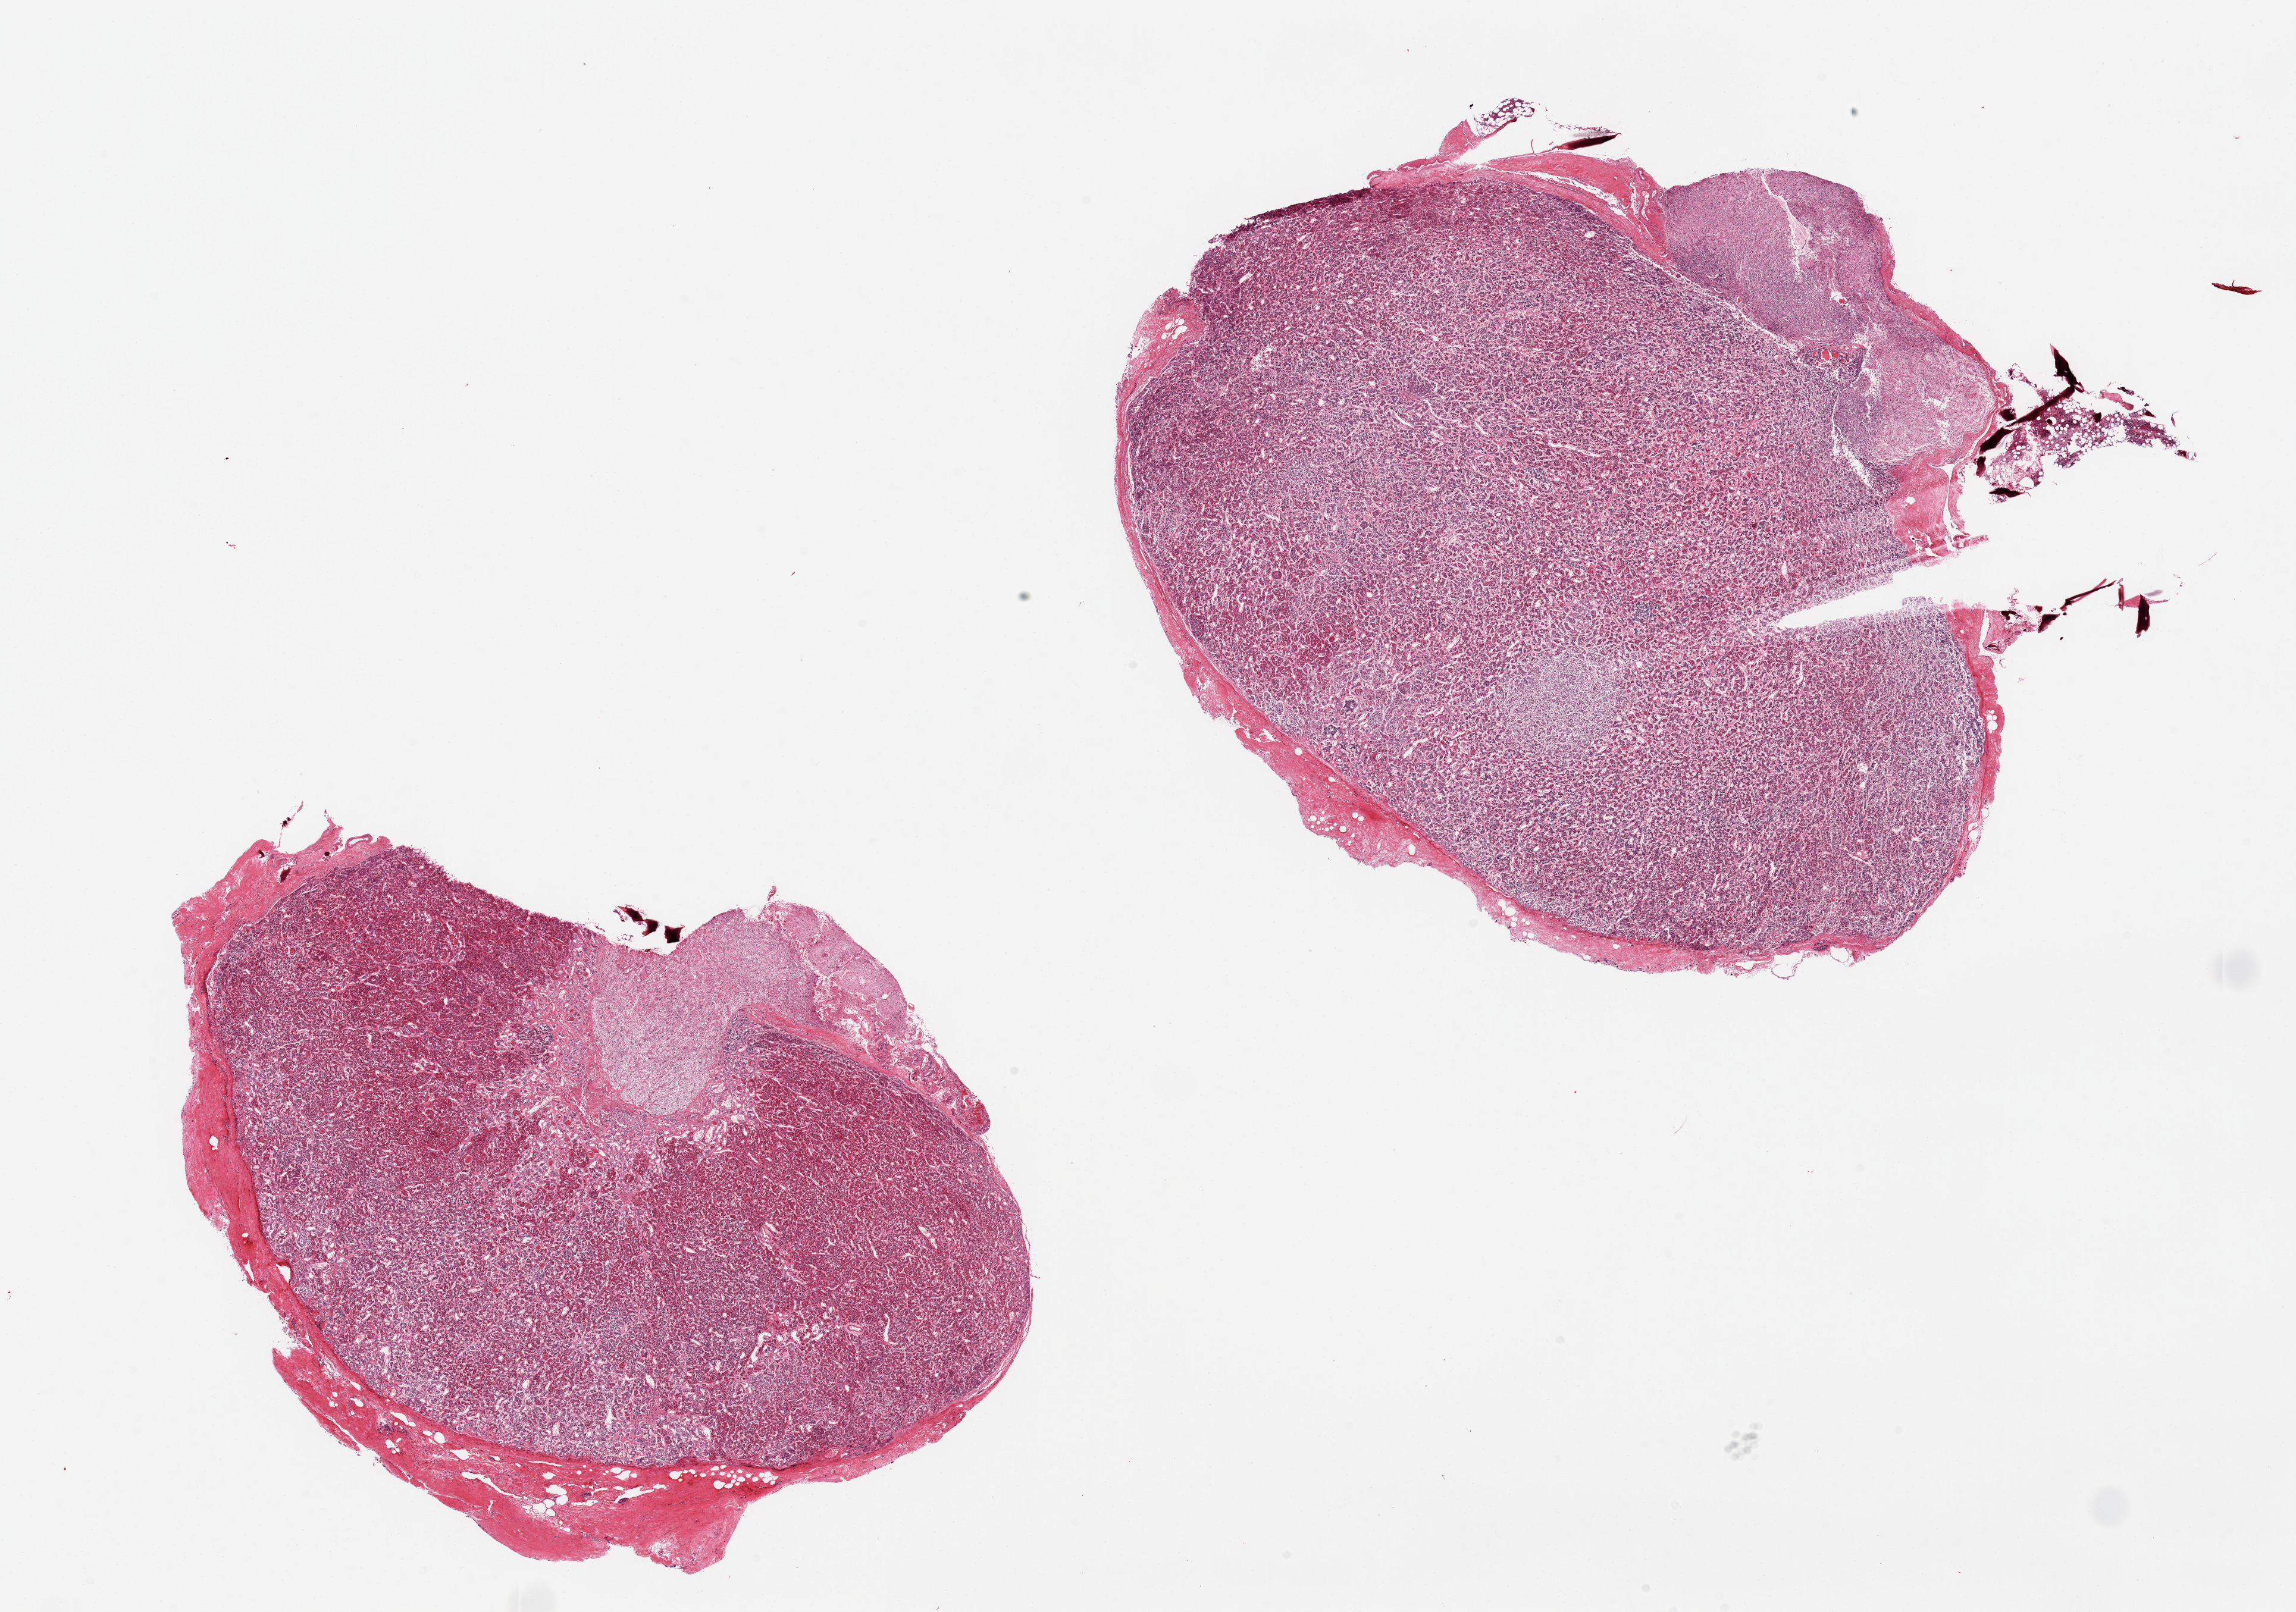
Whole-slide image, haematoxylin and eosin stain, a low-resolution overview of the entire scanned area, about 30.5 x 21.4 mm (from a 20x scan). PAXgene-fixed, paraffin-embedded tissue. Sampled site (target tissue): pituitary. Donor tissue sample. Donor sex: female.
Review note (as recorded): 2 pieces; anterior and posterior represented; some boney fragments with marrow.